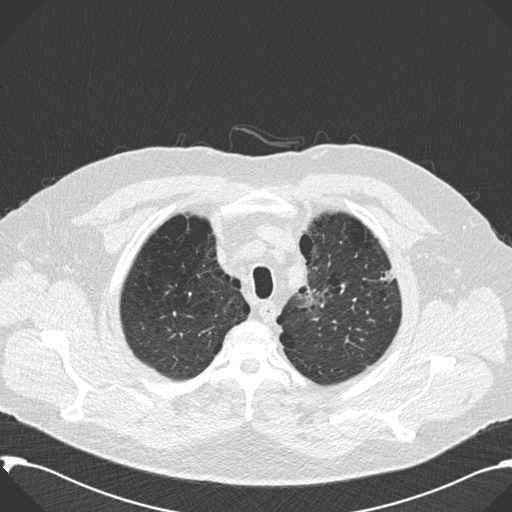
Low-dose screening chest CT, axial slice. Second annual screen. Lung window (W 1500 / L -600 HU). 2 mm slice thickness. Standard (soft-tissue) reconstruction kernel (B30f). 120 kVp. 512 × 512 image matrix. Male, age 59 years at enrolment. Current smoker at enrolment.
Expert-annotated lung lesion, box from (x=368, y=253) to (x=407, y=308) px. Screening reader's record for this exam: no non-calcified nodule ≥4 mm recorded. Later outcome: lung cancer diagnosed 518 days after this screen — bronchiolo-alveolar carcinoma, mixed mucinous and non-mucinous, left upper lobe, stage IA (AJCC 6th edition), 20 mm at pathology.